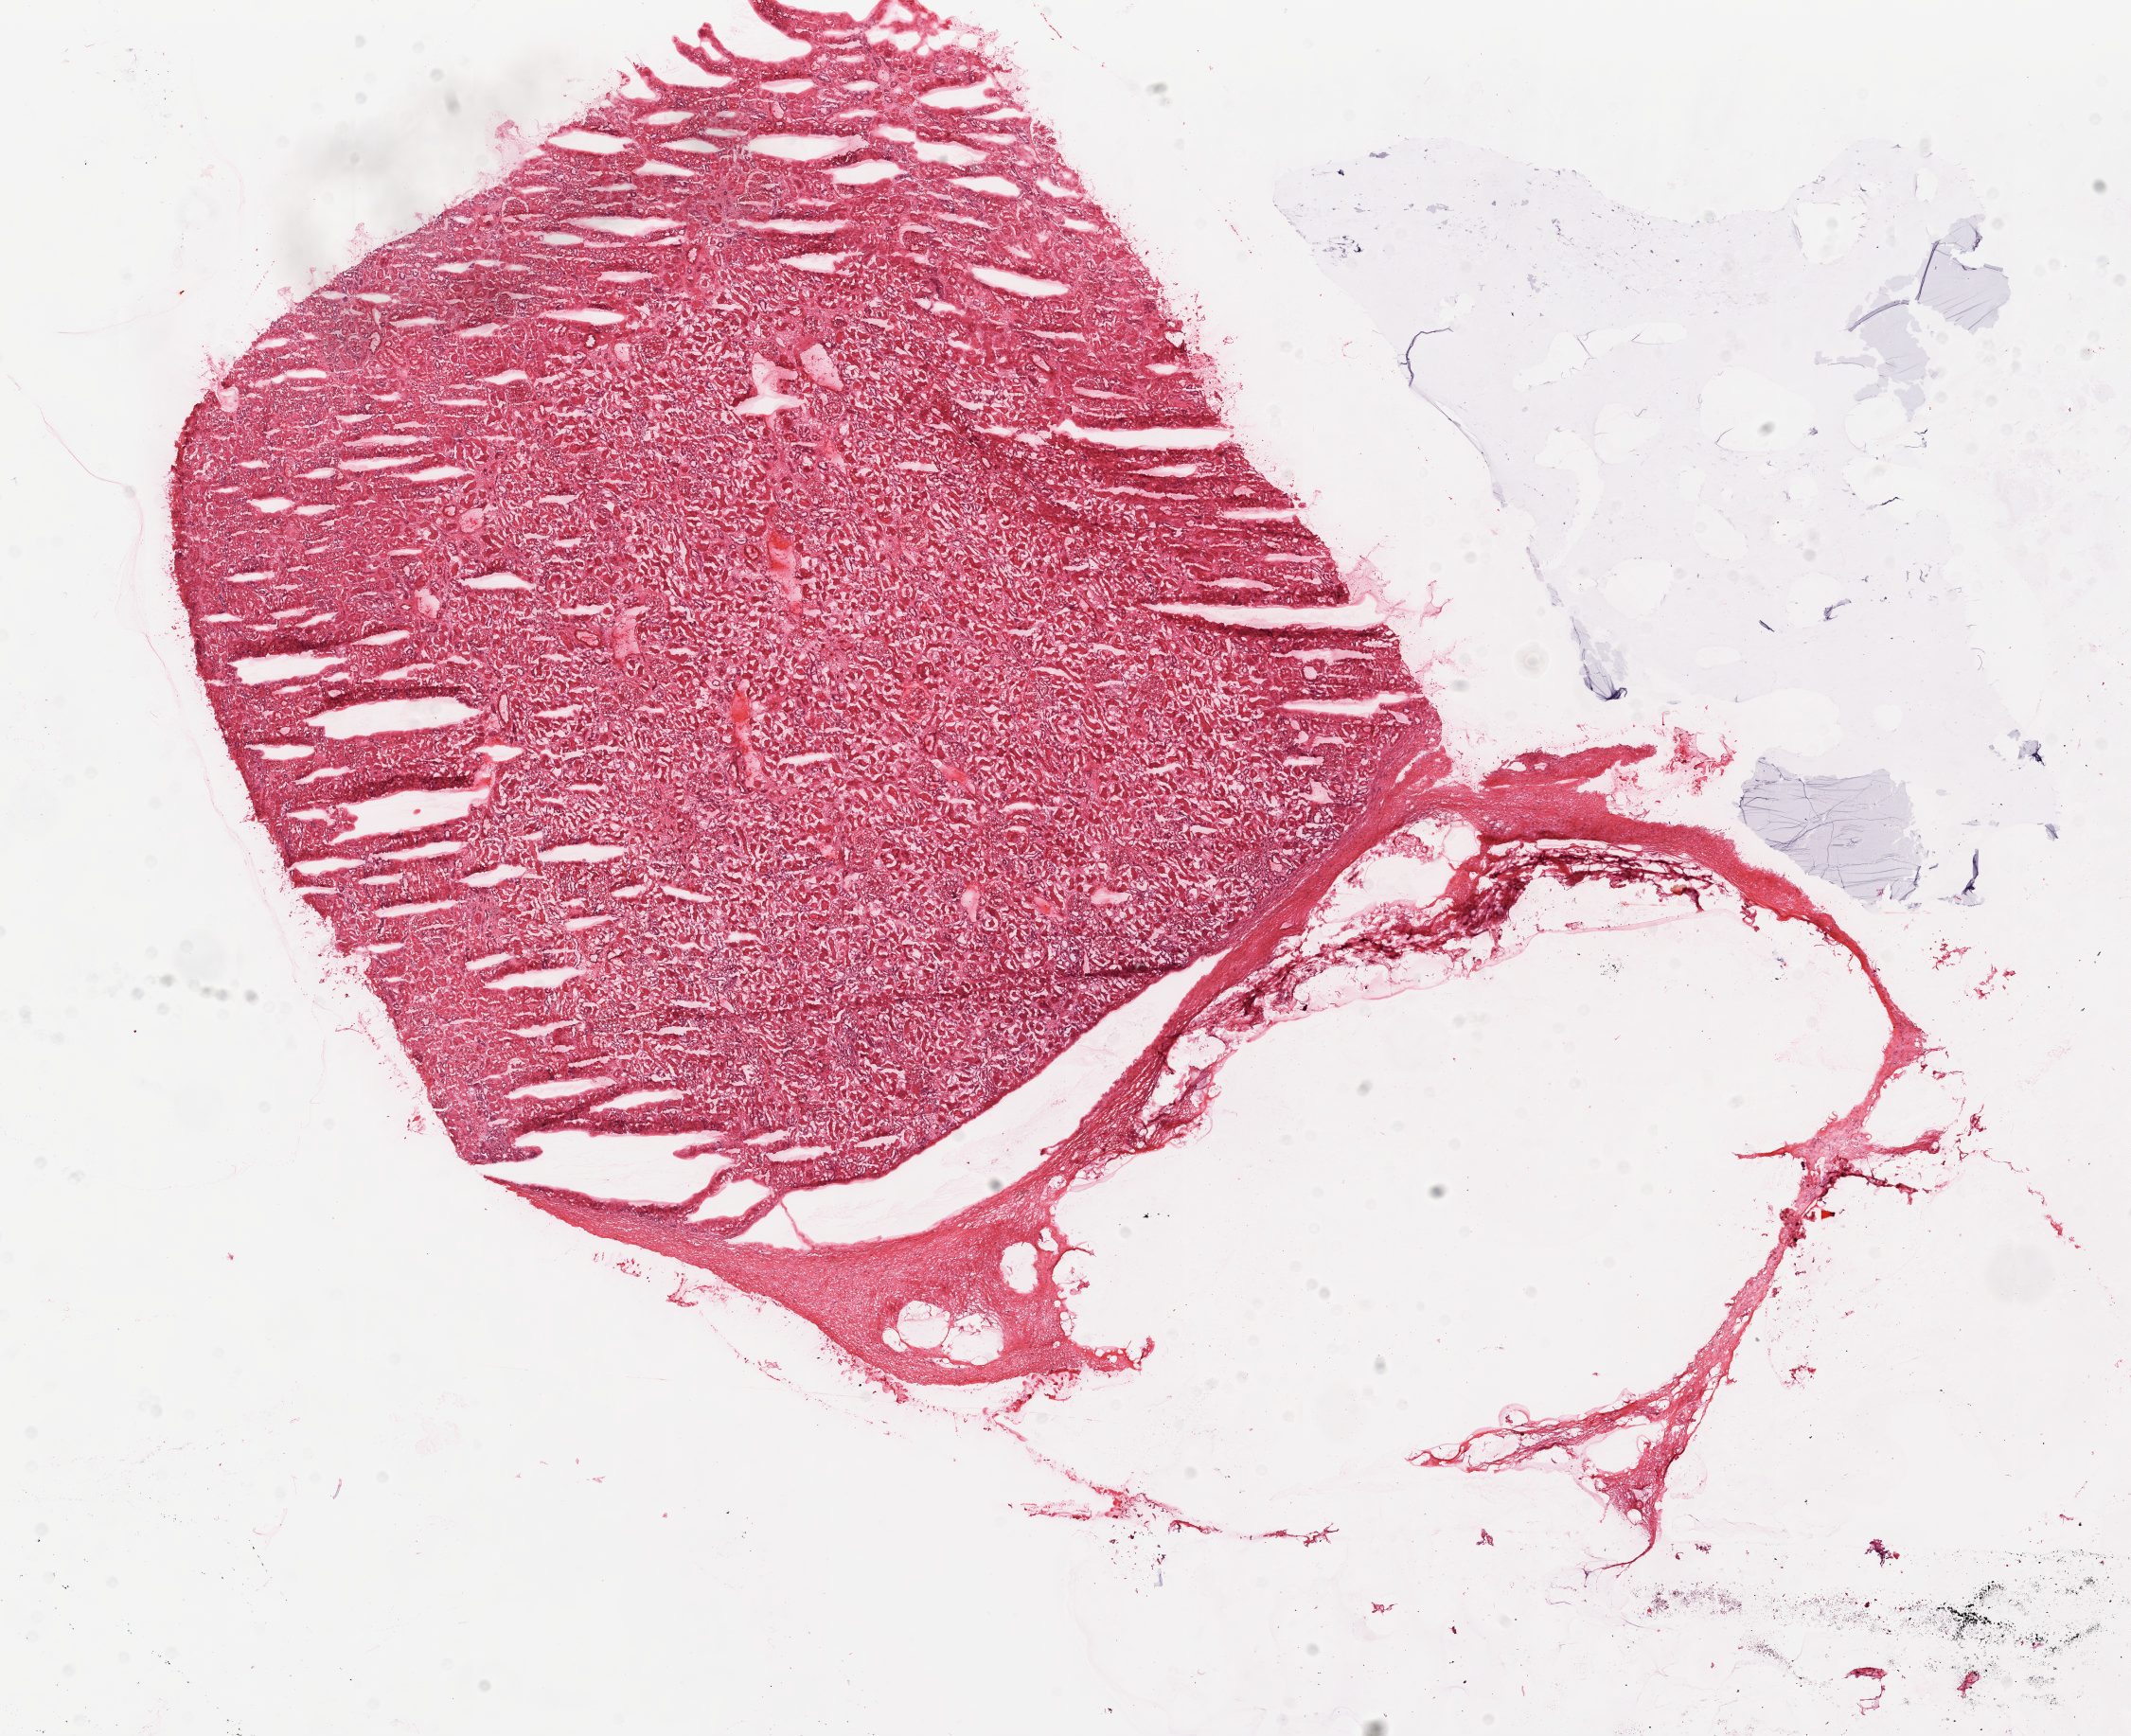
Hematoxylin and eosin (H&E) stained whole-slide image — a low-resolution overview of the entire scanned area, about 17.9 x 14.5 mm (slide scanned at 20x), frozen section from the top of the tissue portion, solid tissue normal (non-tumour tissue) sample from the kidney. Patient: male, age at initial diagnosis 55 years.
This section: solid tissue normal sample (biorepository sample class). Patient diagnosis: Clear cell adenocarcinoma, NOS.